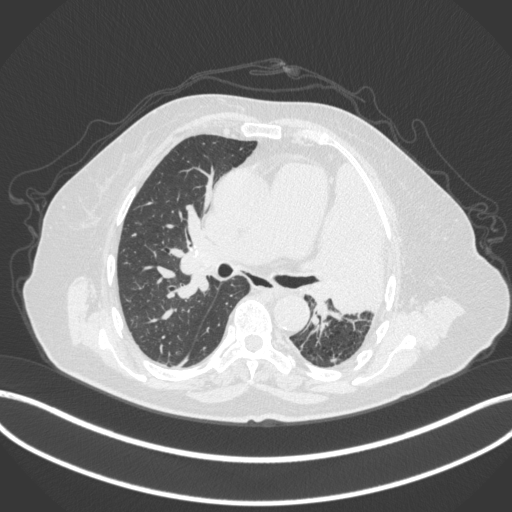
Chest CT, one axial slice; slice 230 of 399 in the series (ordered by position); reconstruction kernel B31f; 120 kVp; lung window (W 1500 / L -600 HU); 1 mm slice thickness; 512 × 512 image matrix, field of view 400 × 400 mm. Female patient, age 75 years. Case-level facts recorded for this patient, not image findings: clinical TNM (as recorded): T3 N3 M1.
Outlined on this slice (bounding box drawn by a radiologist):
- lung tumour (recorded histology: adenocarcinoma): box from (x=315, y=157) to (x=381, y=325) px